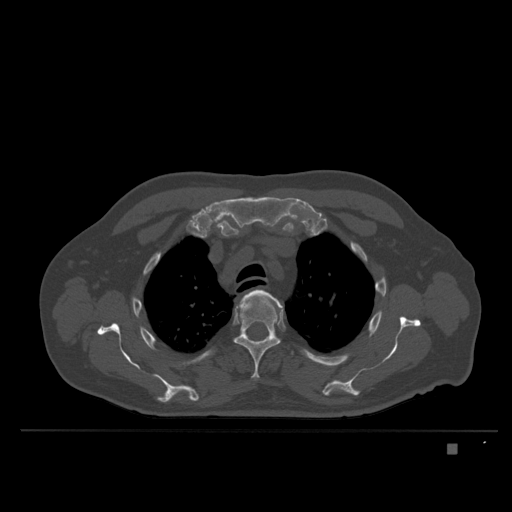
CT including the spine, one axial slice; position 288 of 435 along the scan axis; bone window (W 1800 / L 400 HU); 1.5 mm slice thickness; 512 × 512 image matrix, field of view 434 × 434 mm. Male patient, age 73 years. Case-level facts recorded for this patient, not image findings: primary cancer: skin.
Outlined on this slice (semi-automatically segmented with operator editing):
- T3 vertebra: bounding box (x1, y1, x2, y2) in pixels: (243, 289, 283, 308)
- T4 vertebra: (234, 296, 280, 381)
- T5 vertebra: (291, 351, 294, 354)